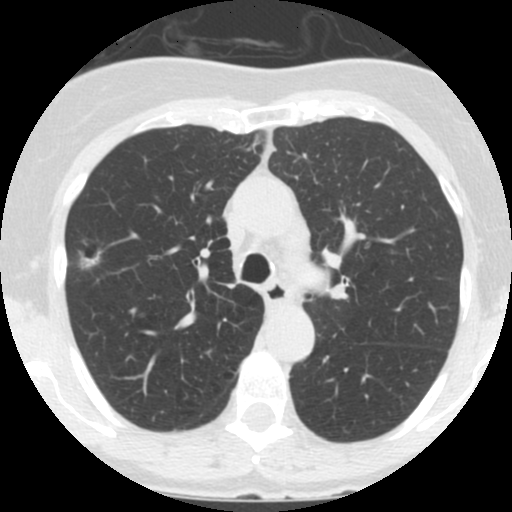
Low-dose screening chest CT, one axial slice; position 99 of 146 along the scan axis; reconstruction kernel STANDARD; 120 kVp; lung window (W 1500 / L -600 HU); 2.5 mm slice thickness; 512 × 512 image matrix, field of view 280 × 280 mm.
Structures marked on this image (outlined manually by an expert reader):
- lesion 1 (tumor, upper lobe of right lung): bounding box (x1, y1, x2, y2) in pixels: (79, 250, 100, 269)